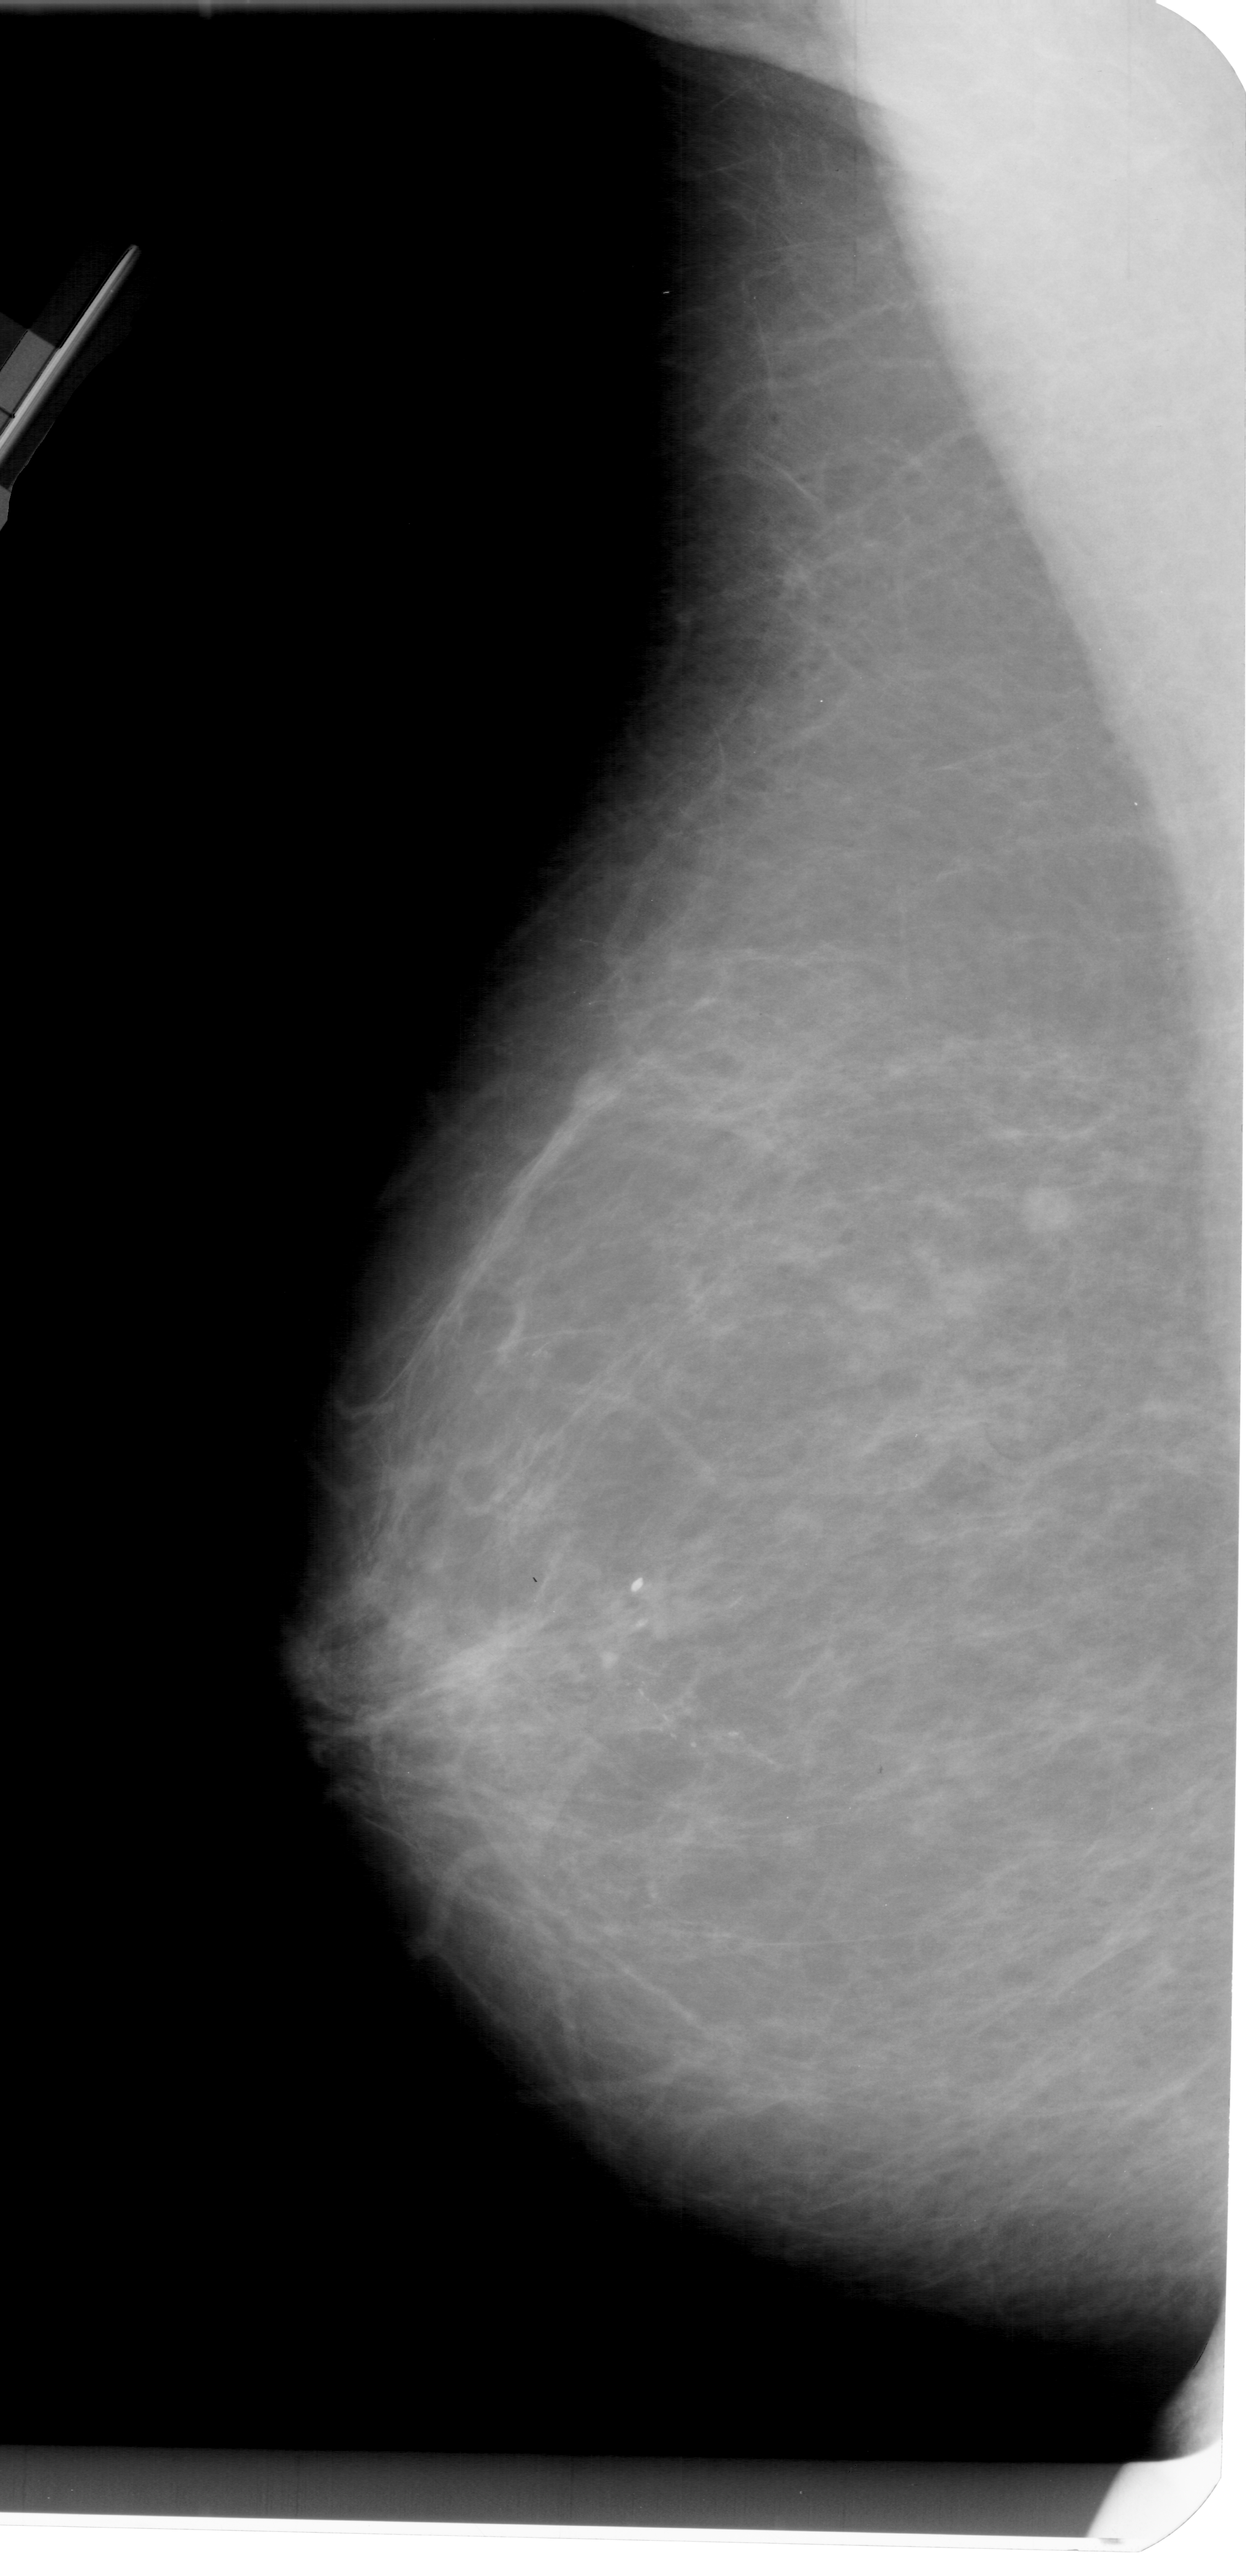
Digitized screen-film mammogram, left breast, MLO view, BI-RADS breast density category 2 (scale 1–4).
Marked abnormality: calcifications, morphology pleomorphic, distribution linear; BI-RADS assessment category 4; subtlety rating 4 on a 1 (subtle) to 5 (obvious) scale; pathology result (as recorded, not read from the image): malignant.